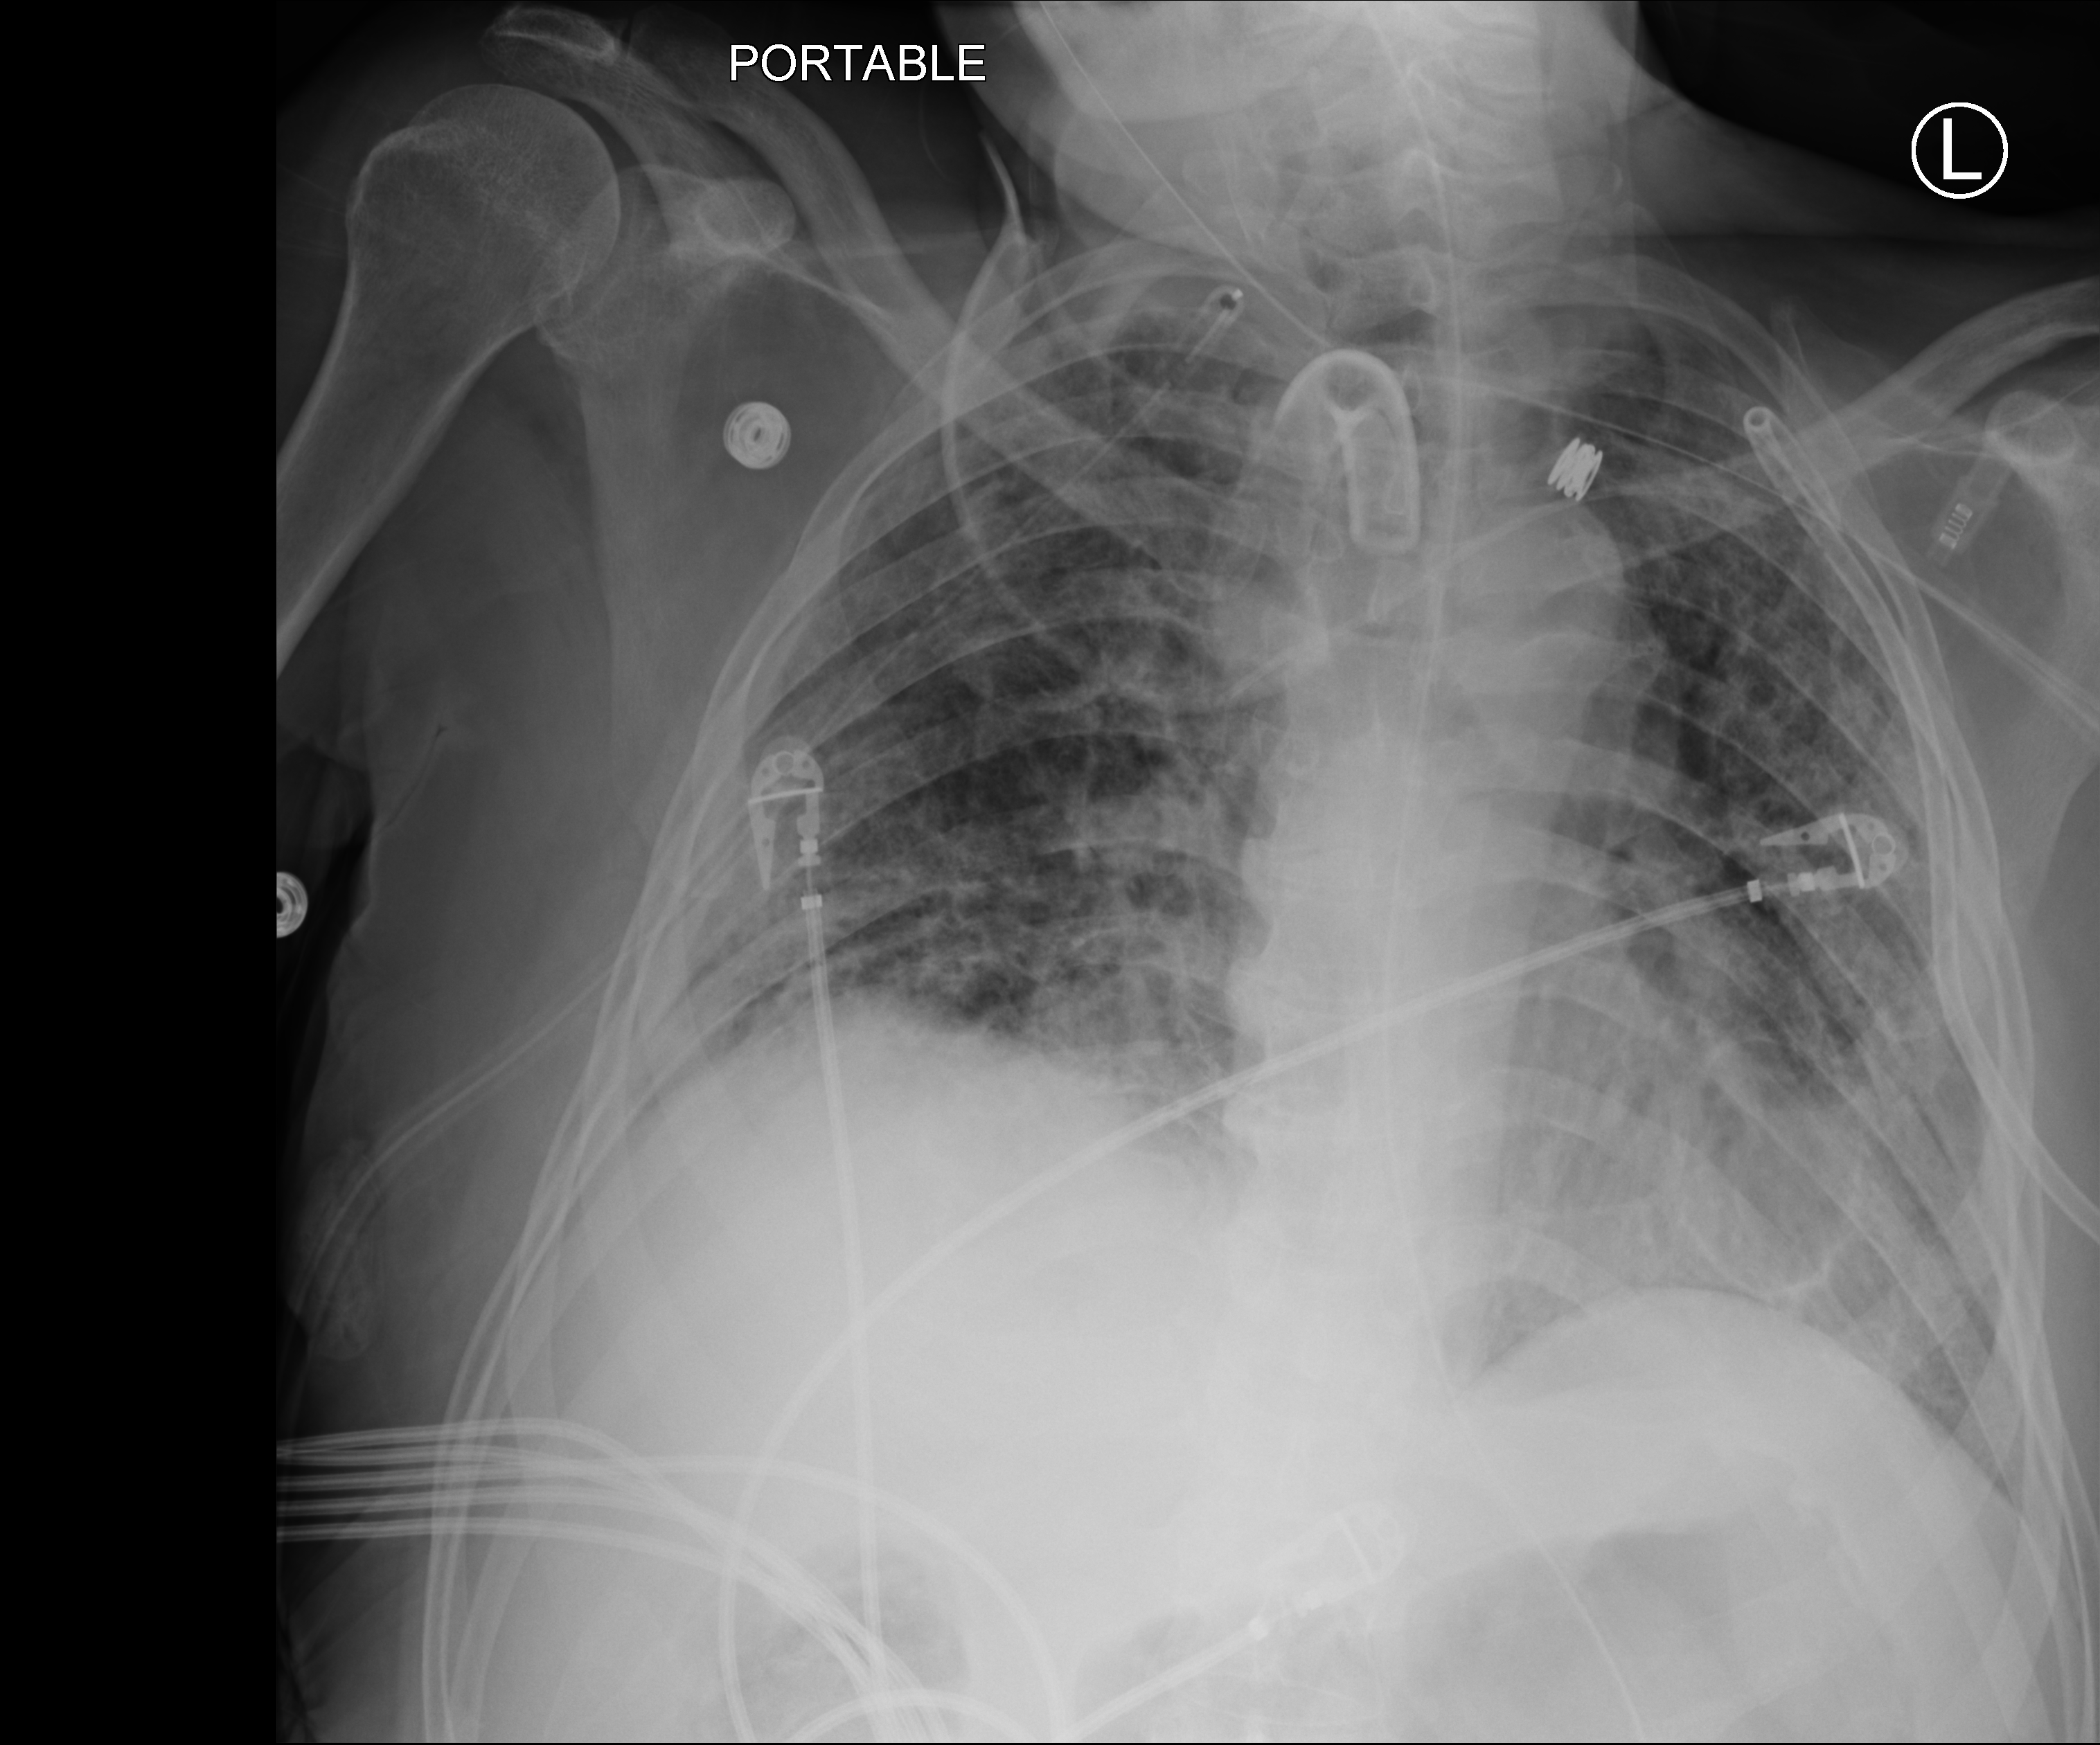
Chest X-ray (portable). Patient hospitalised with COVID-19; male, aged 18–59 years.
From the hospital-stay record, not from the radiograph (when in the stay this image was taken is not recorded): admitted to intensive care during this hospital stay: yes.